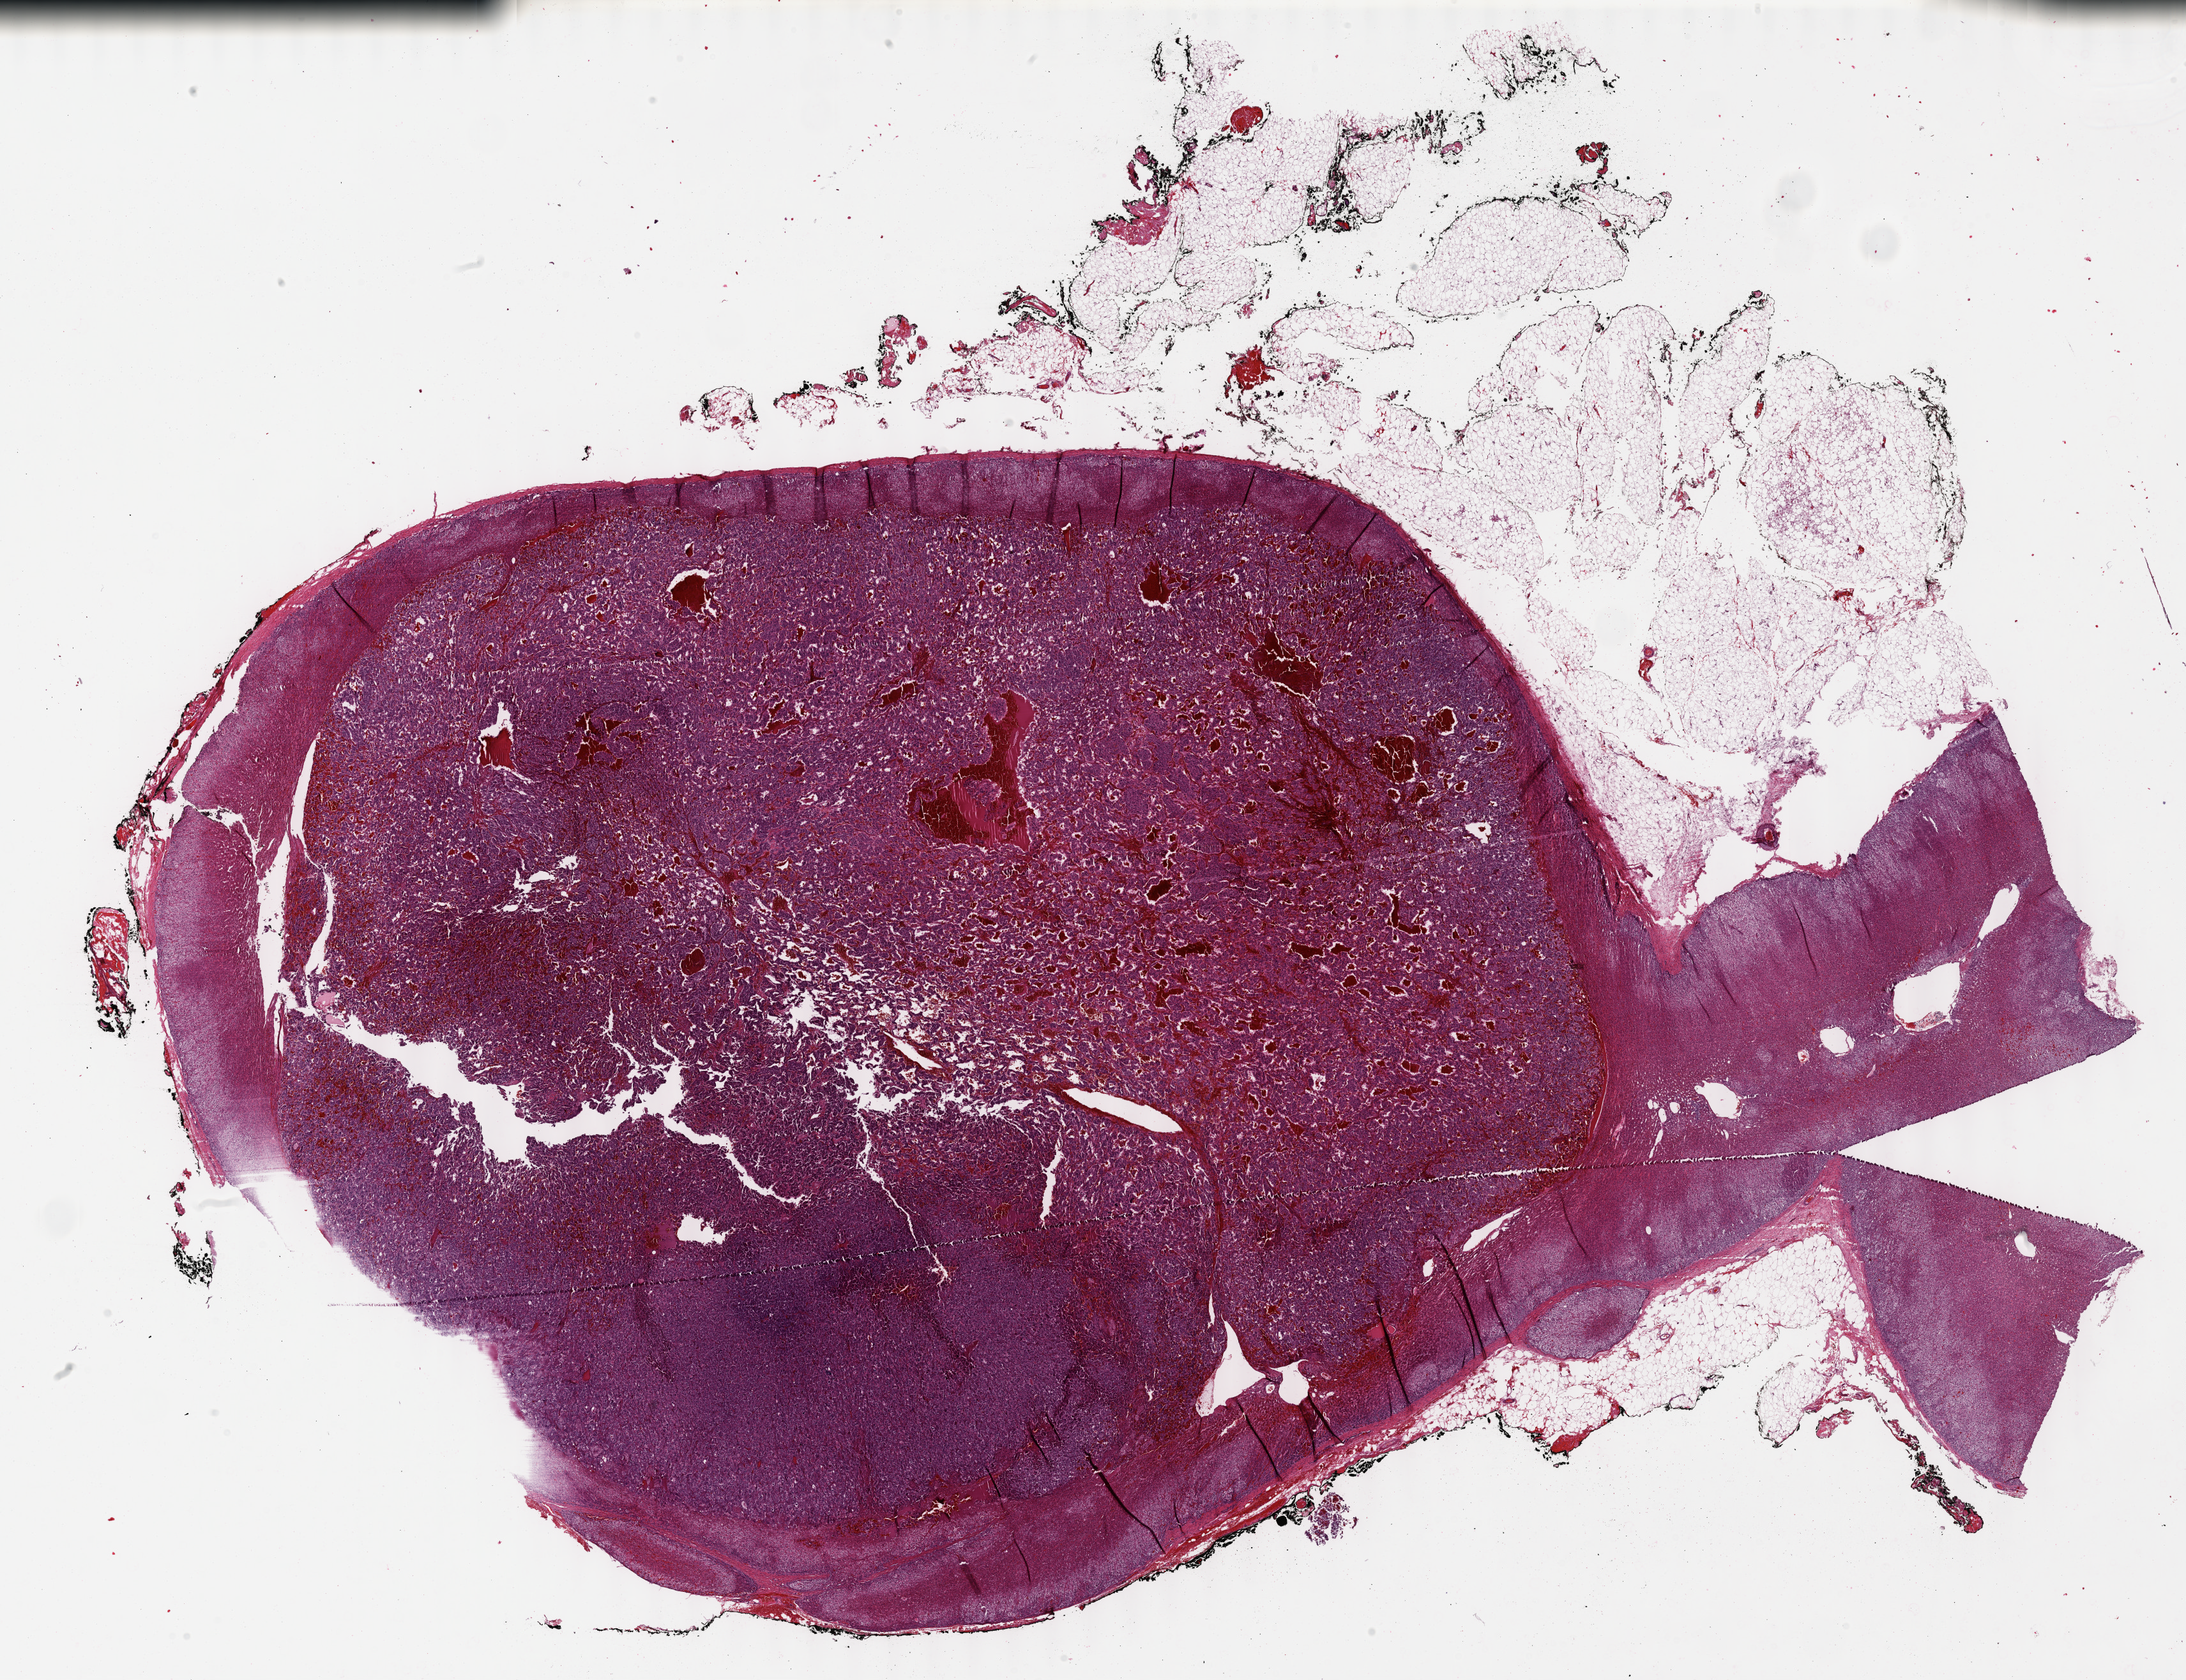
Whole-slide histology image, H&E-stained — a low-resolution overview of the entire scanned area, about 27.7 x 21.3 mm (slide scanned at 40x); FFPE section; sample: primary tumour, adrenal gland. Female, age 28 years at initial diagnosis.
Histologic diagnosis: Pheochromocytoma, NOS.